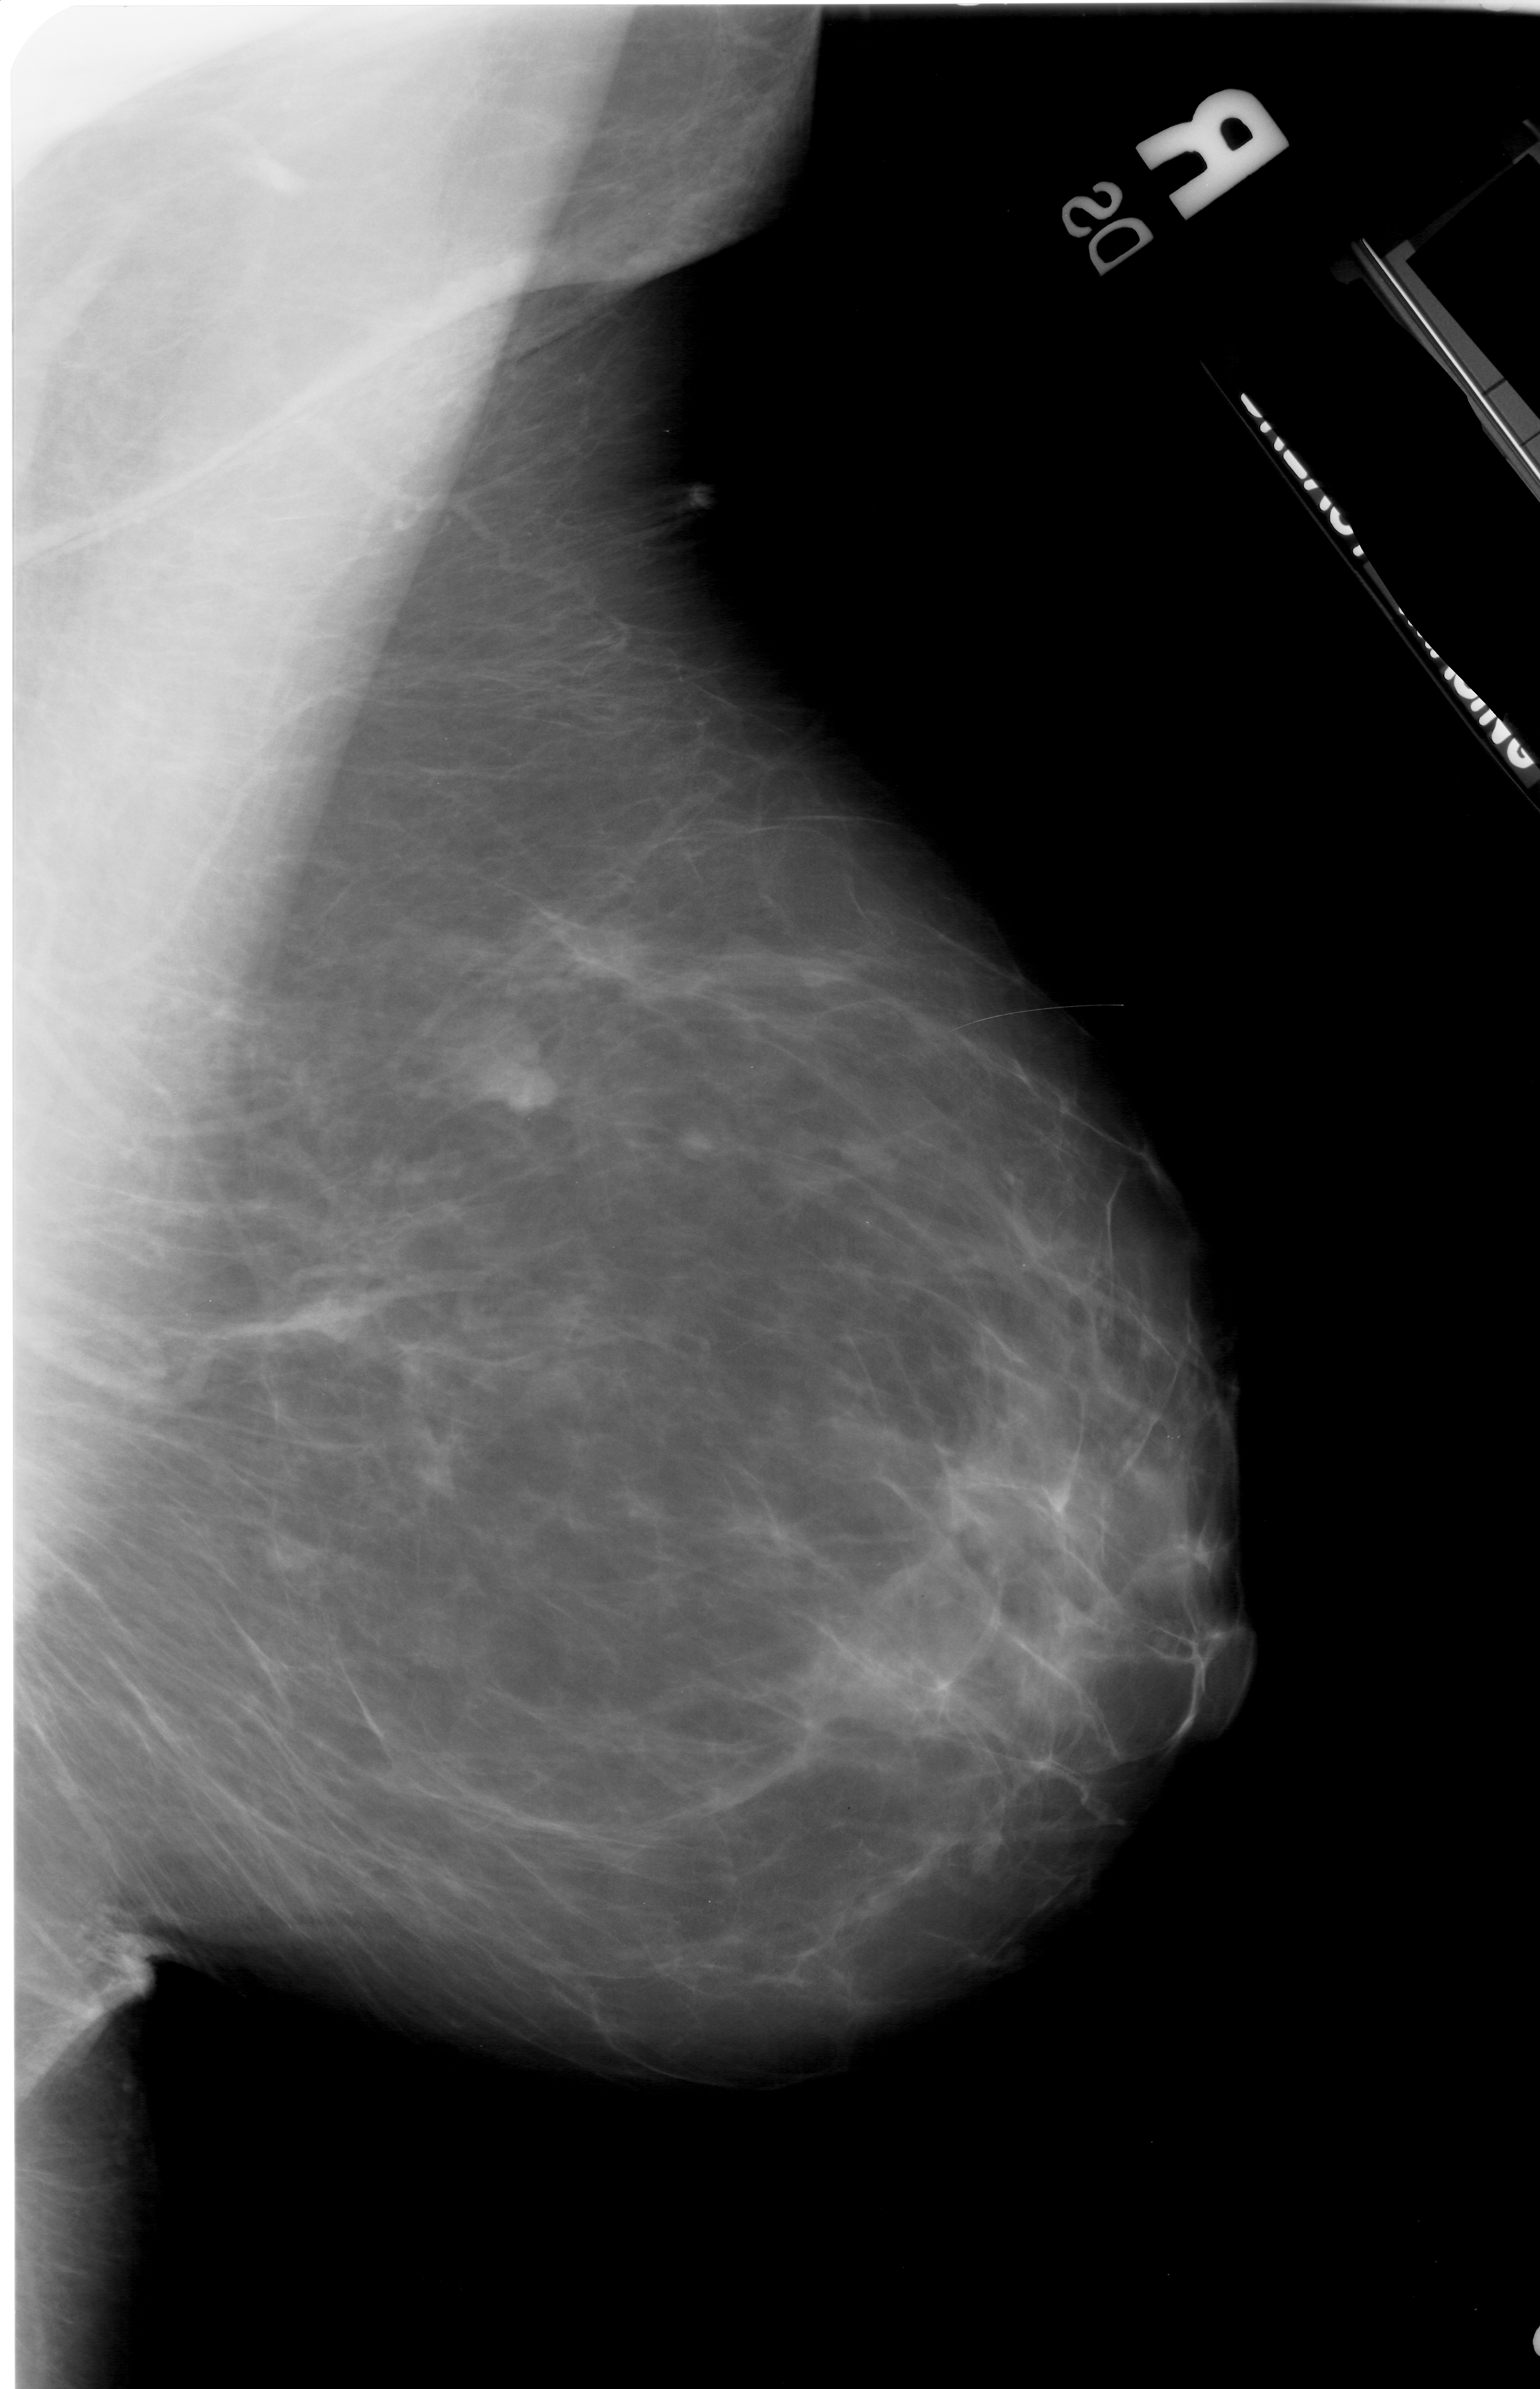
Scanned film-screen mammogram. Right breast. MLO view. Breast composition: almost entirely fatty (BI-RADS density category 1 of 4). 1540 × 2389 image matrix.
Expert-marked regions of interest on this image (one box per marked abnormality):
- mass, shape lobulated, margins obscured; BI-RADS assessment category 3; pathology result (as recorded, not read from the image): benign: bounding box <464,1041,560,1119> (left, top, right, bottom; pixels)